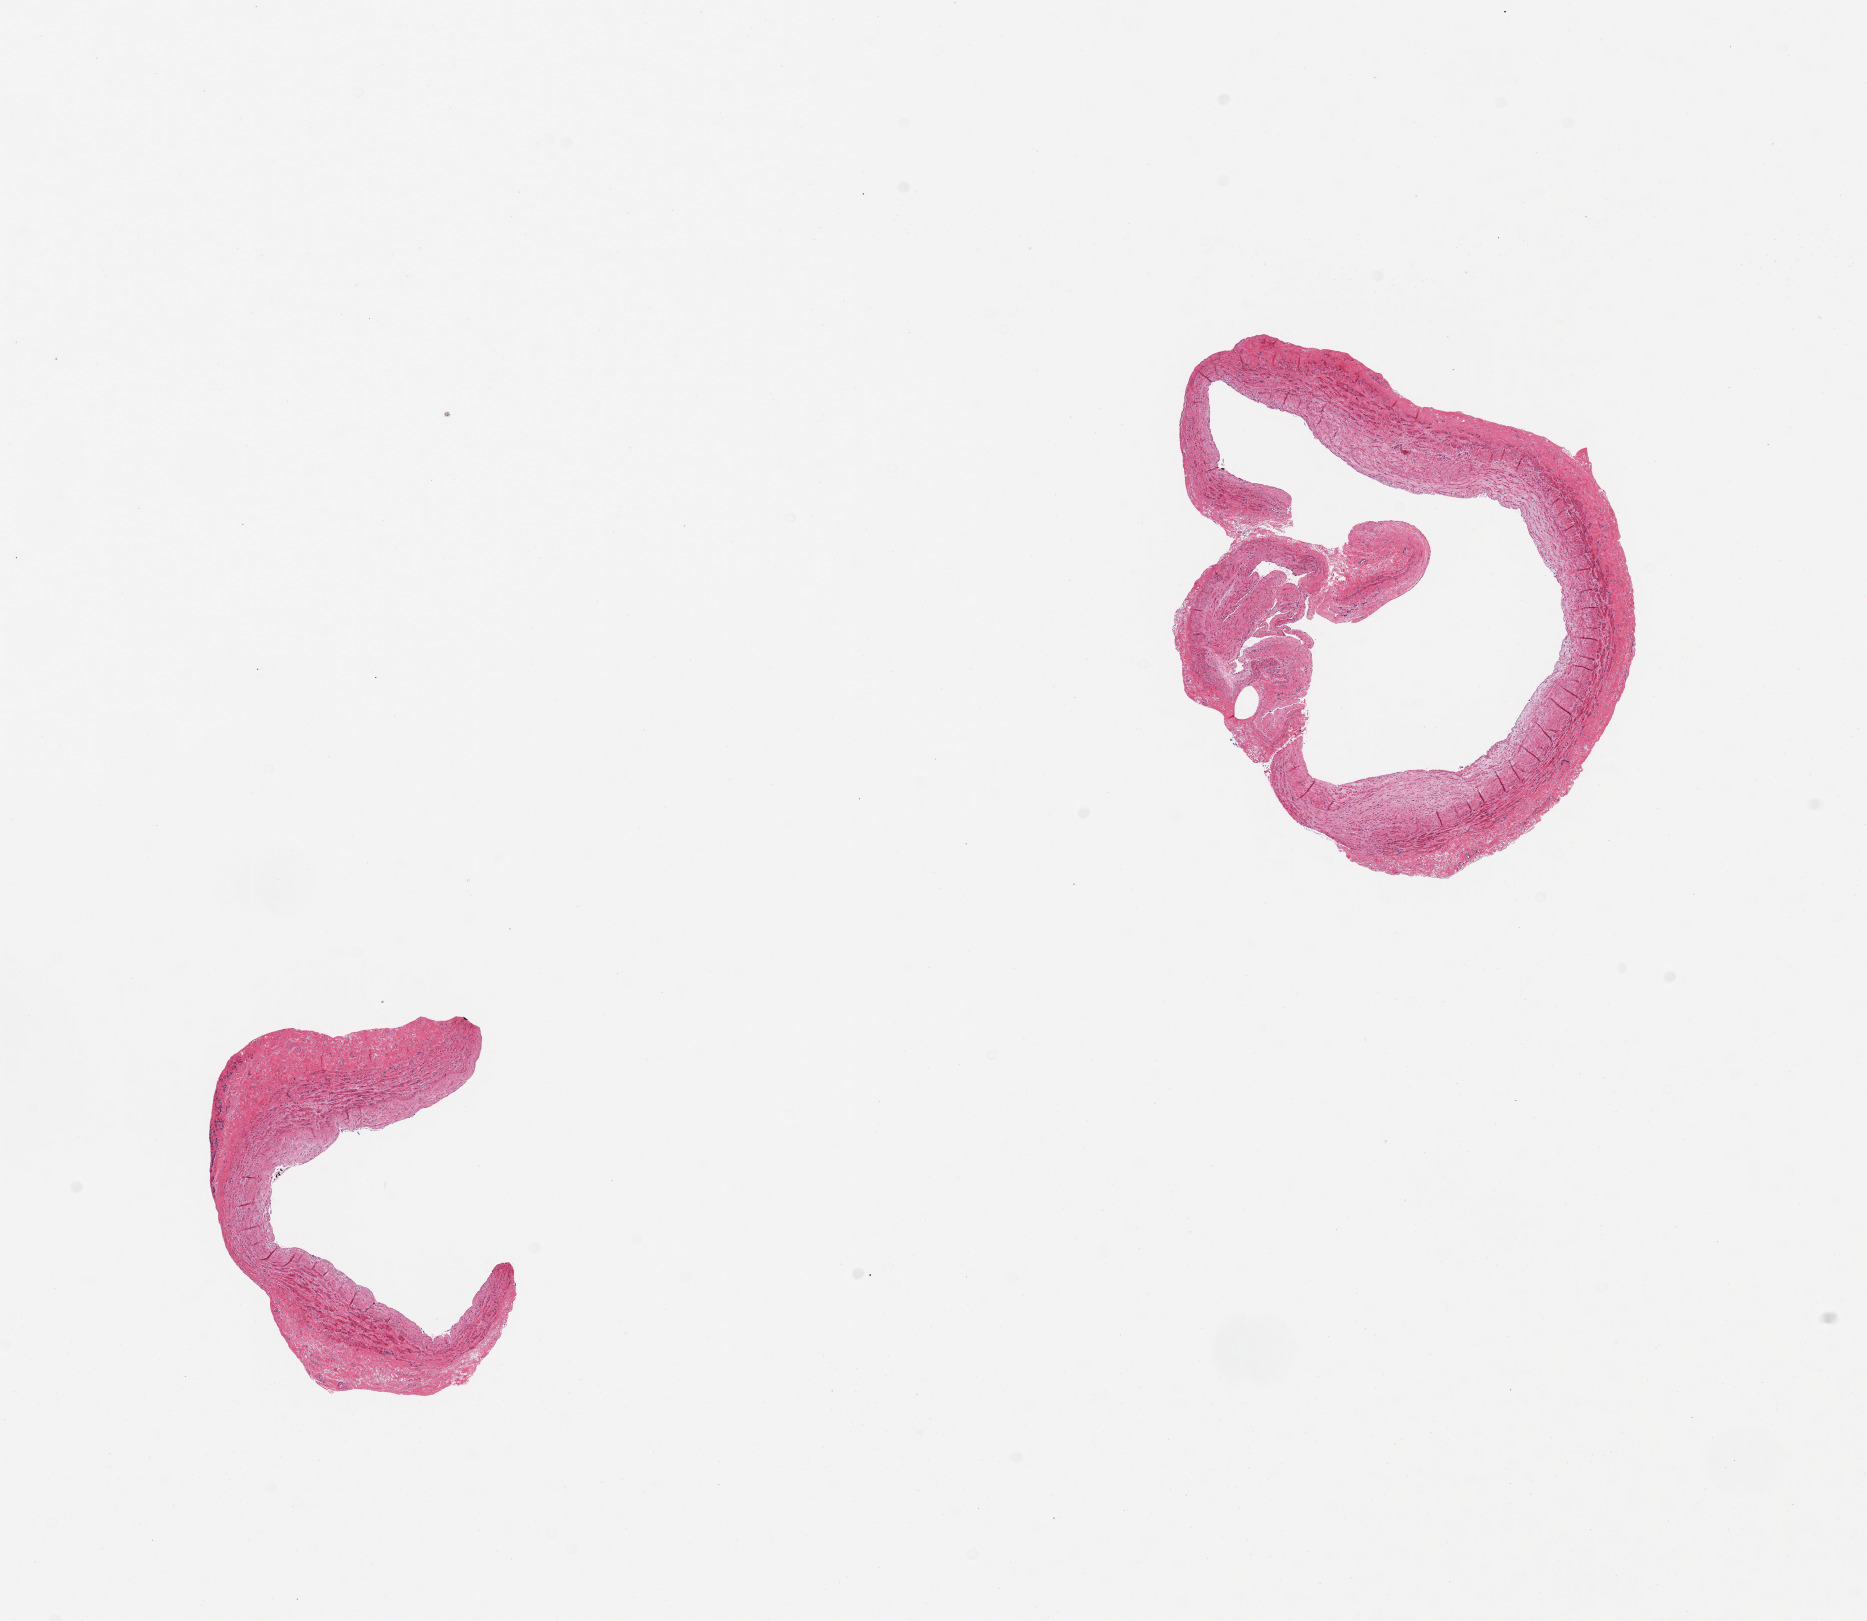
Digitized H&E-stained section, brightfield — whole scanned area (about 14.8 x 12.8 mm) shown as a low-resolution overview. PAXgene-fixed, paraffin-embedded tissue. Section of tibial artery (target tissue). Donor tissue sample. Donor sex: male.
Reviewer comment on this tissue sample: 2 pieces, confirmed target muscular artery, no significant atherosis/adherent fat.